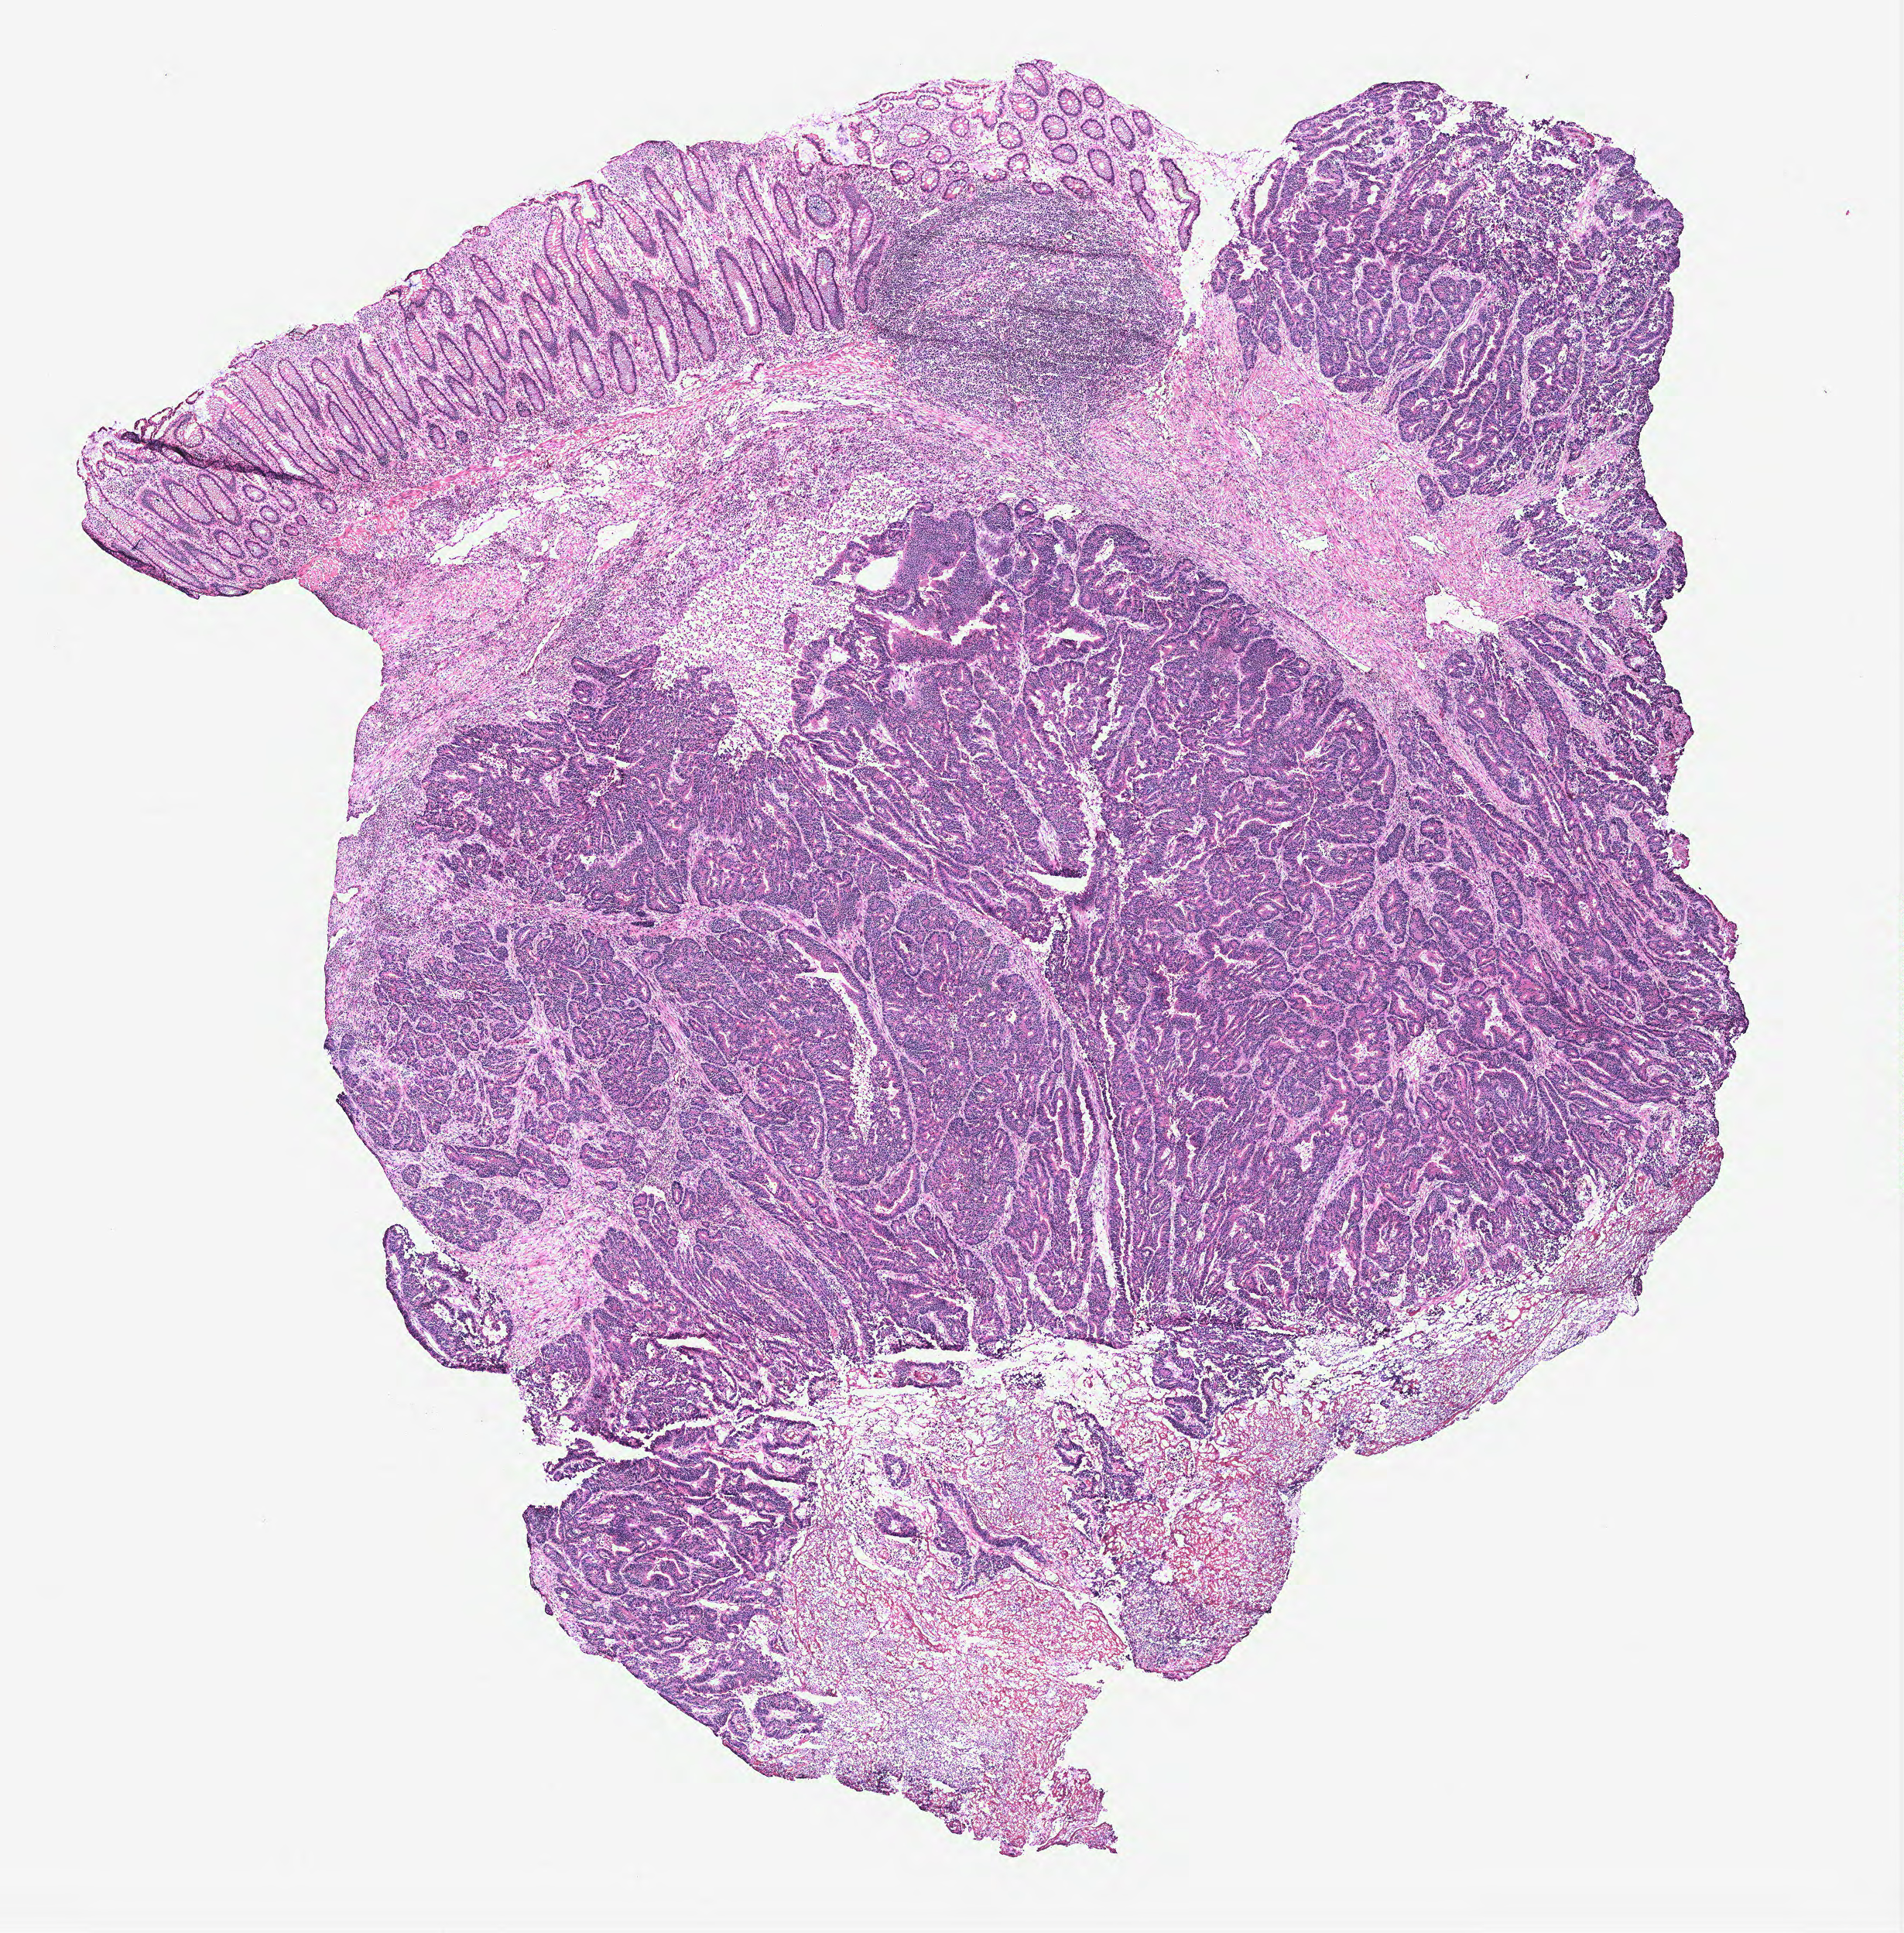
Whole-slide histology image, H&E, whole scanned area (about 9.8 x 10.0 mm, slide scanned at 40x) shown as a low-resolution overview; colon, normal (non-tumour) tissue. Patient: female, age 66 years.
- this section: normal (non-tumour) tissue from the same patient
- patient diagnosis: Adenocarcinoma, NOS